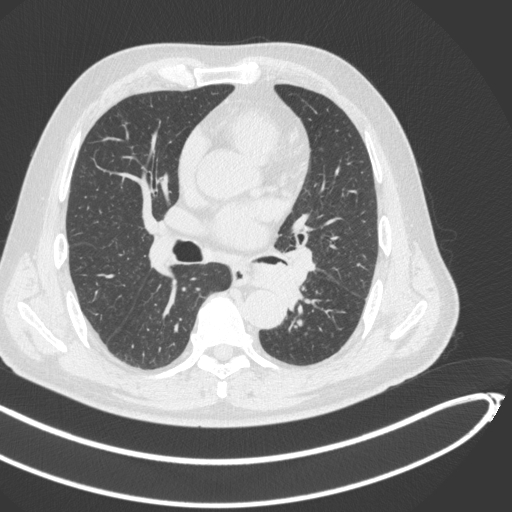
Chest CT, one axial slice. Position 252 of 466 along the scan axis. Reconstruction kernel B31f. 120 kVp. Lung window (W 1500 / L -600 HU). 1 mm slice thickness. 512 × 512 image matrix, field of view 400 × 400 mm. Male patient, age 64 years. Case-level facts recorded for this patient, not image findings: clinical TNM (as recorded): T1c N0 M0.
Annotated regions visible in this slice (bounding box drawn by a radiologist):
- lung tumour (recorded histology: squamous cell carcinoma): bounding box <250,257,311,310> (left, top, right, bottom; pixels)